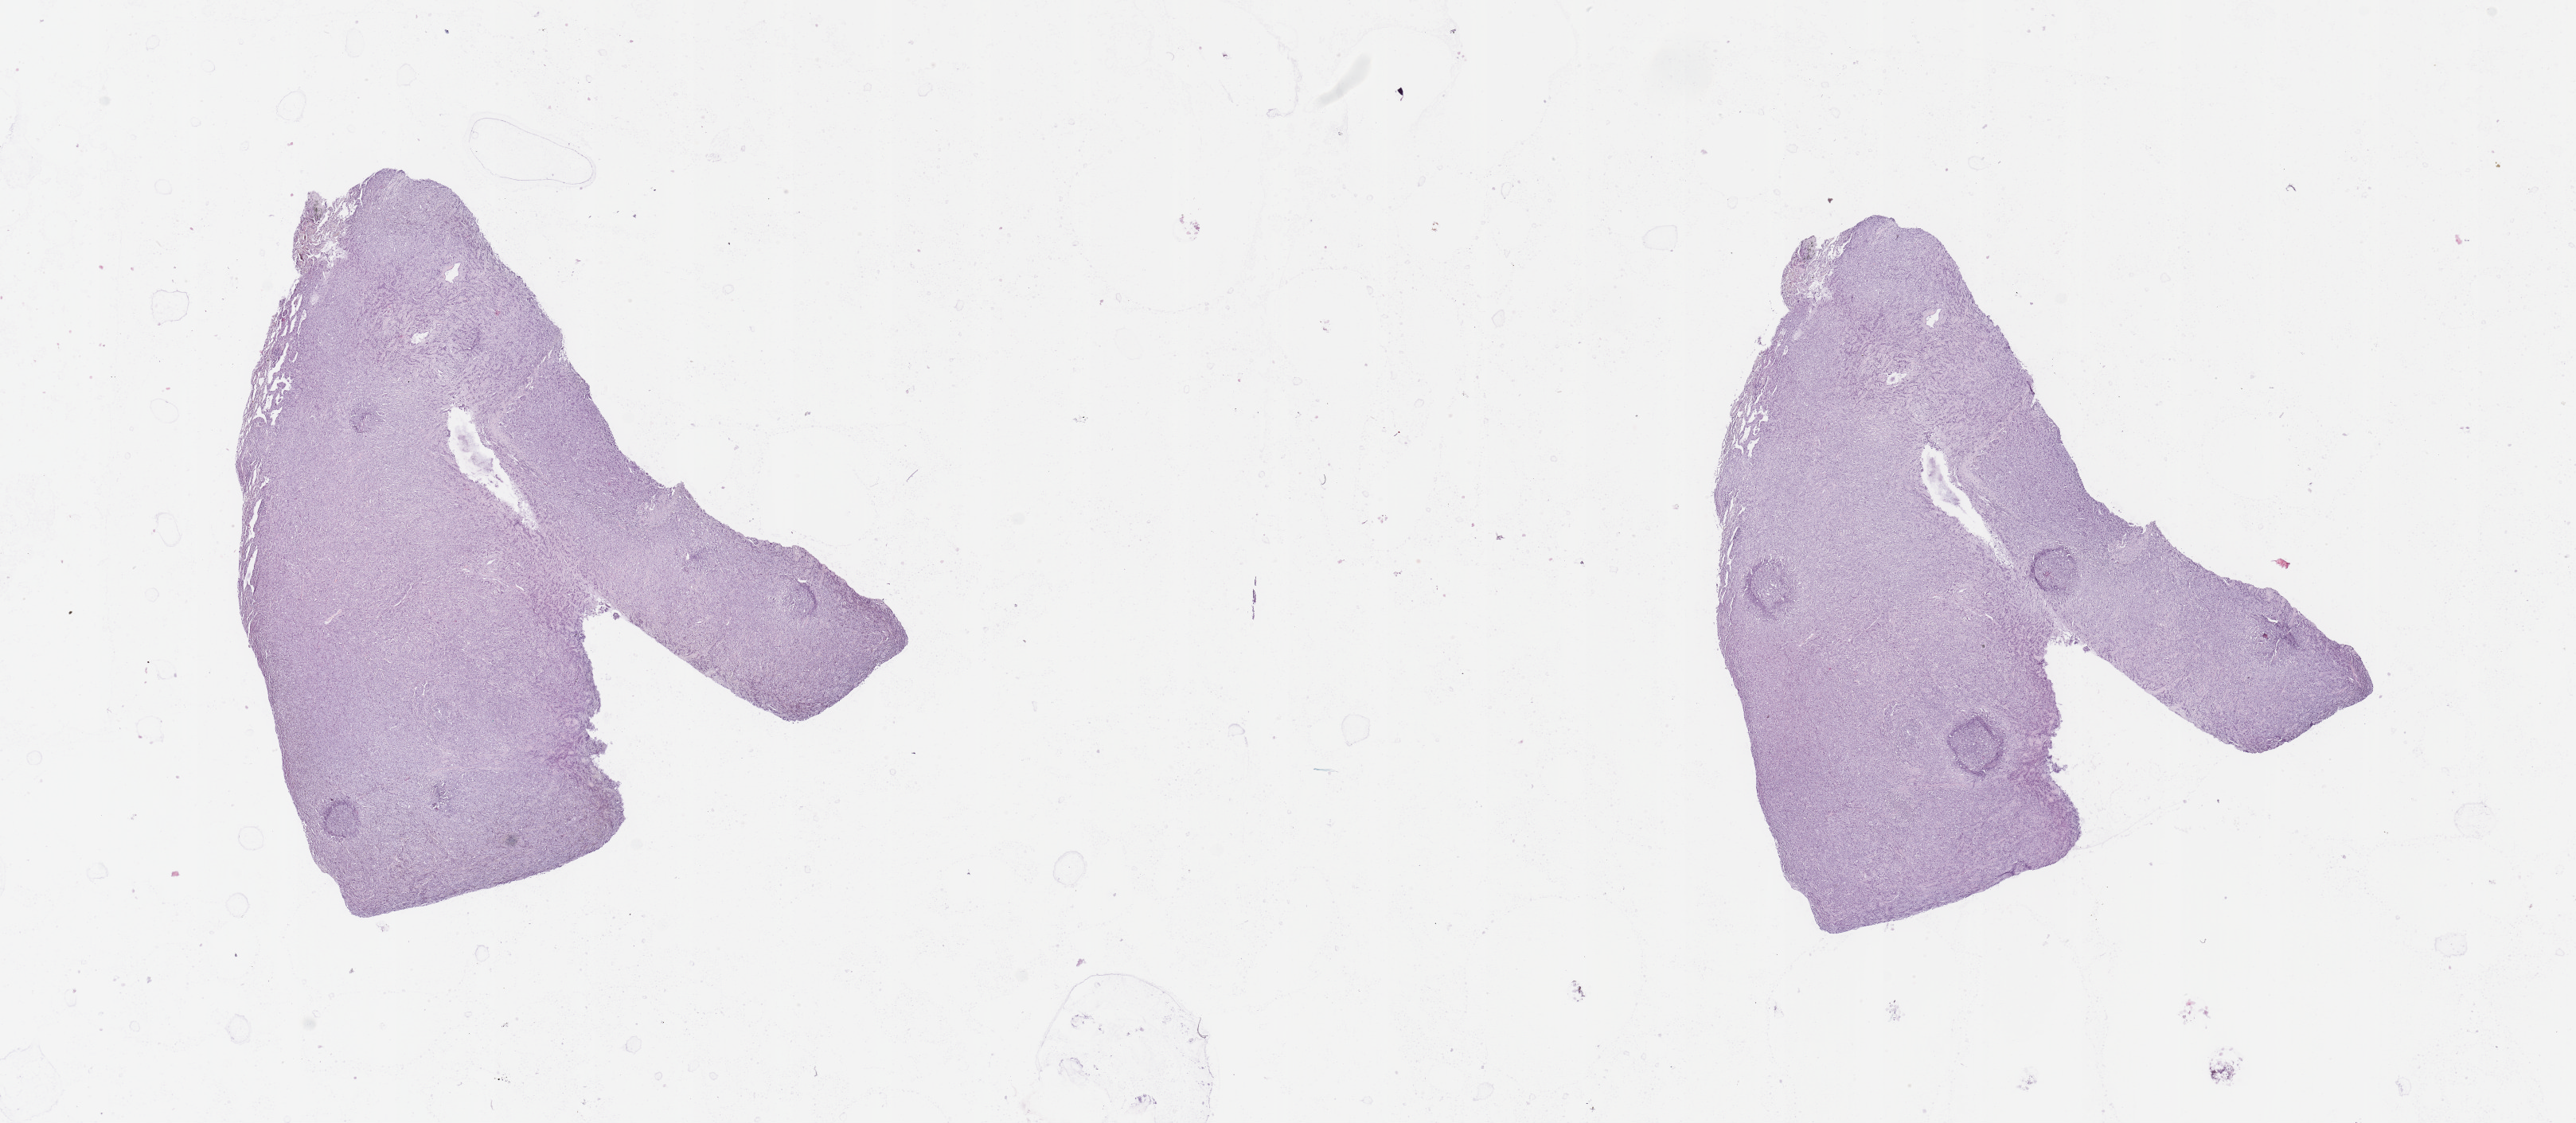
Digitized Hematoxylin and eosin (H&E) stained tissue section (whole slide), low-resolution overview of the scanned area, about 25.6 x 11.2 mm, tumour tissue sample, sampled site: lung. Male, 51 y/o. Pathologist review of this section (percent, as recorded): tumour nuclei 85%, necrosis 0%.
Histologic diagnosis: Squamous cell carcinoma, NOS.